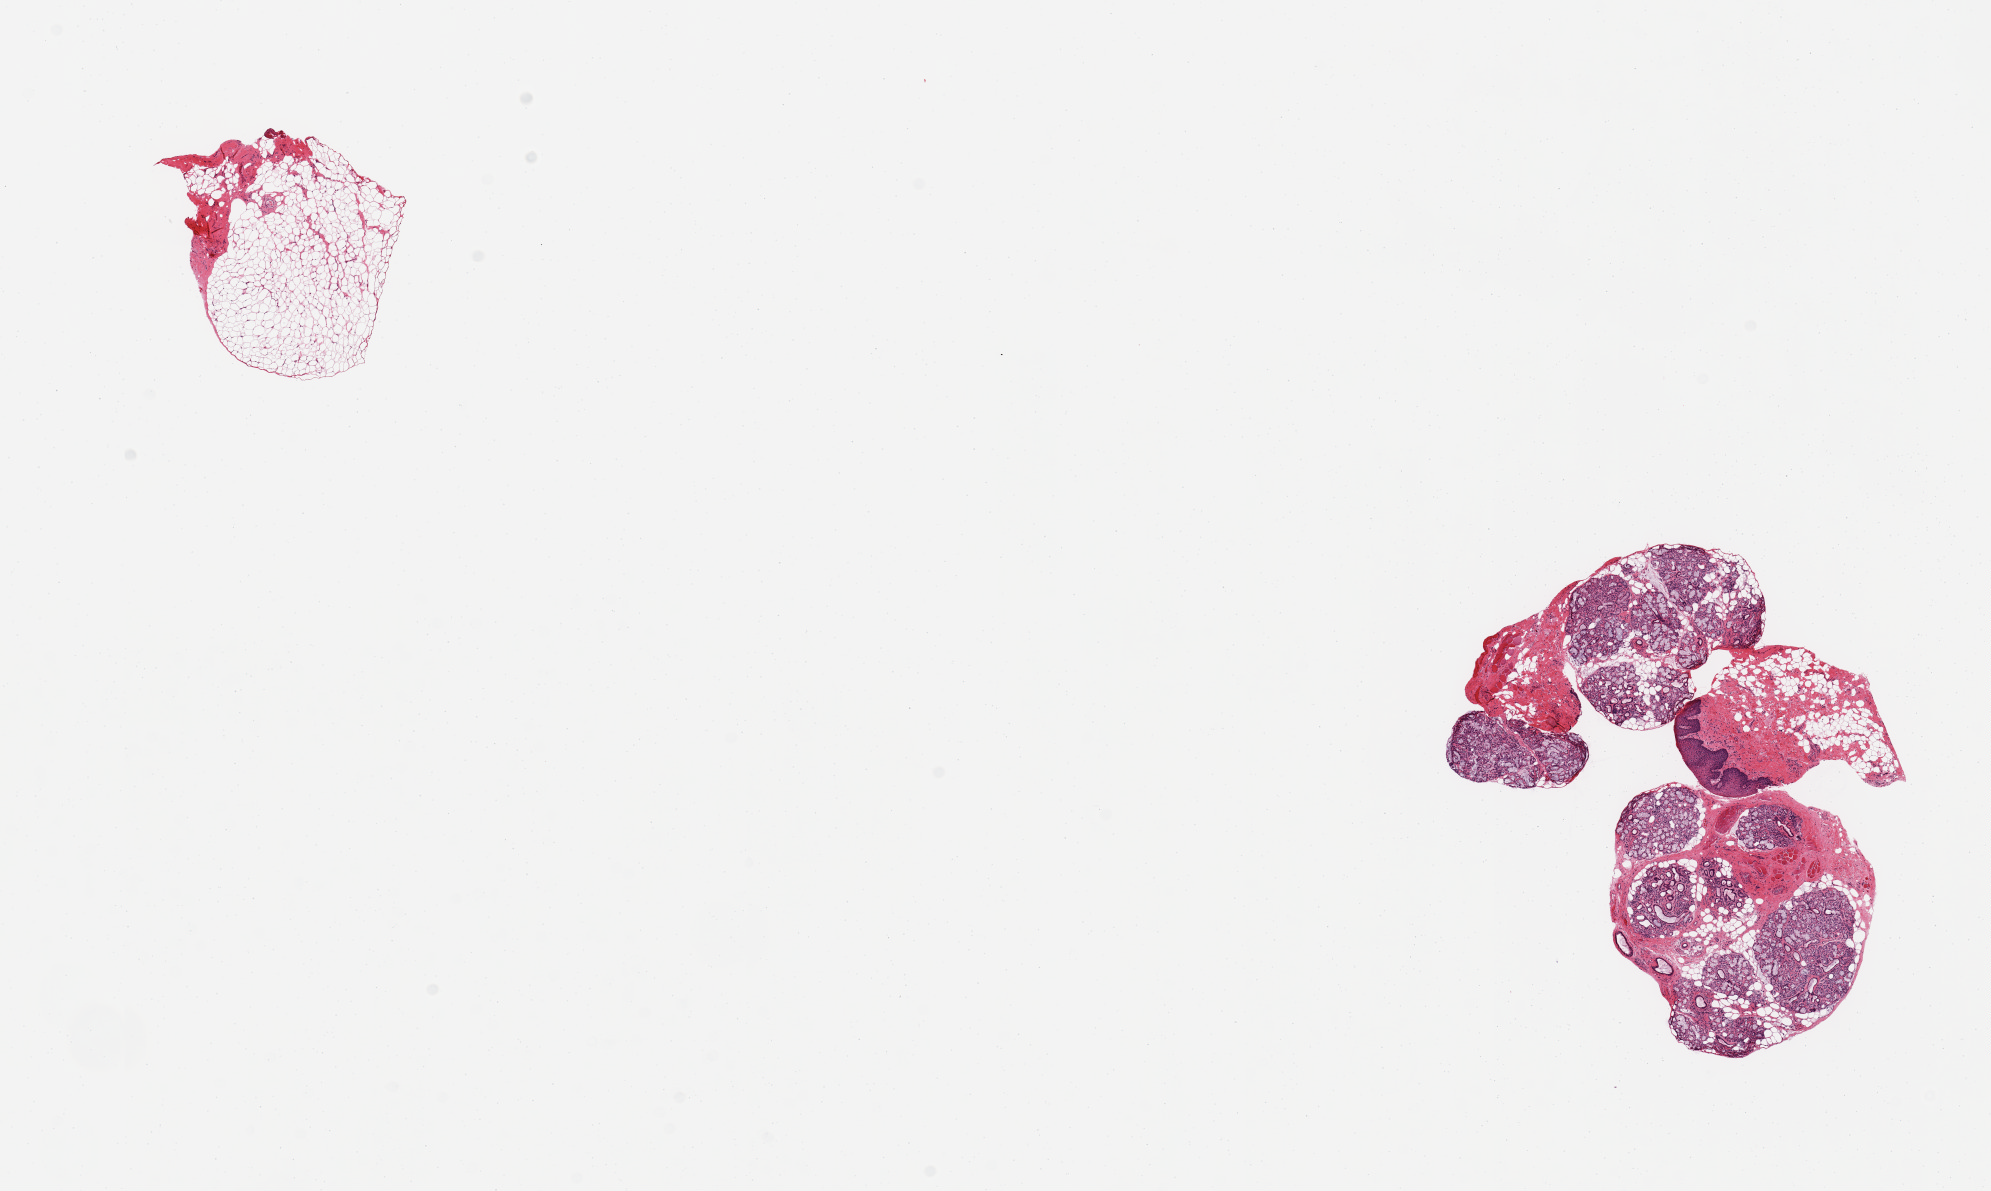
Haematoxylin and eosin whole-slide image, whole scanned area (about 15.8 x 9.4 mm, from a 20x scan) shown as a low-resolution overview; PAXgene-fixed, paraffin-embedded tissue; target tissue: minor salivary gland; tissue donor sample. Donor sex: male.
Review note (as recorded): 2 pieces; one piece fibroadipose tissue only; second piece salivary gland with attached squamous mucosa and musculo- fibro-adipose tissue.